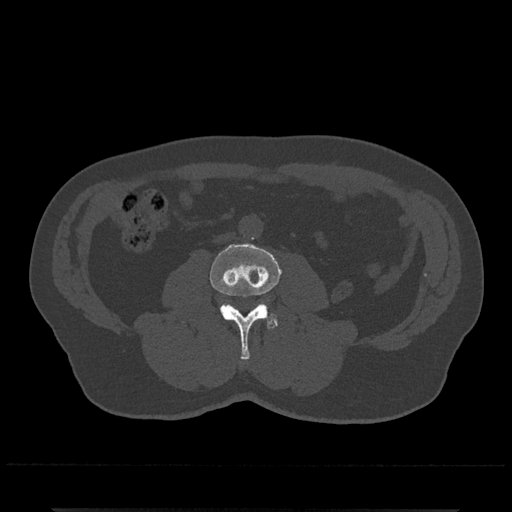
CT including the spine, one axial slice; position 211 of 797 along the scan axis; 120 kVp; bone window (W 1800 / L 400 HU); 0.5 mm slice thickness; 512 × 512 image matrix, field of view 393 × 393 mm. Male patient, age 67 years. From the clinical record (not read from this slice): primary cancer: prostate.
Structures marked on this image (semi-automatically segmented with operator editing):
- L3 vertebra: bounding box [x1, y1, x2, y2] px = [210, 244, 281, 360]
- L4 vertebra: [263, 303, 278, 326]